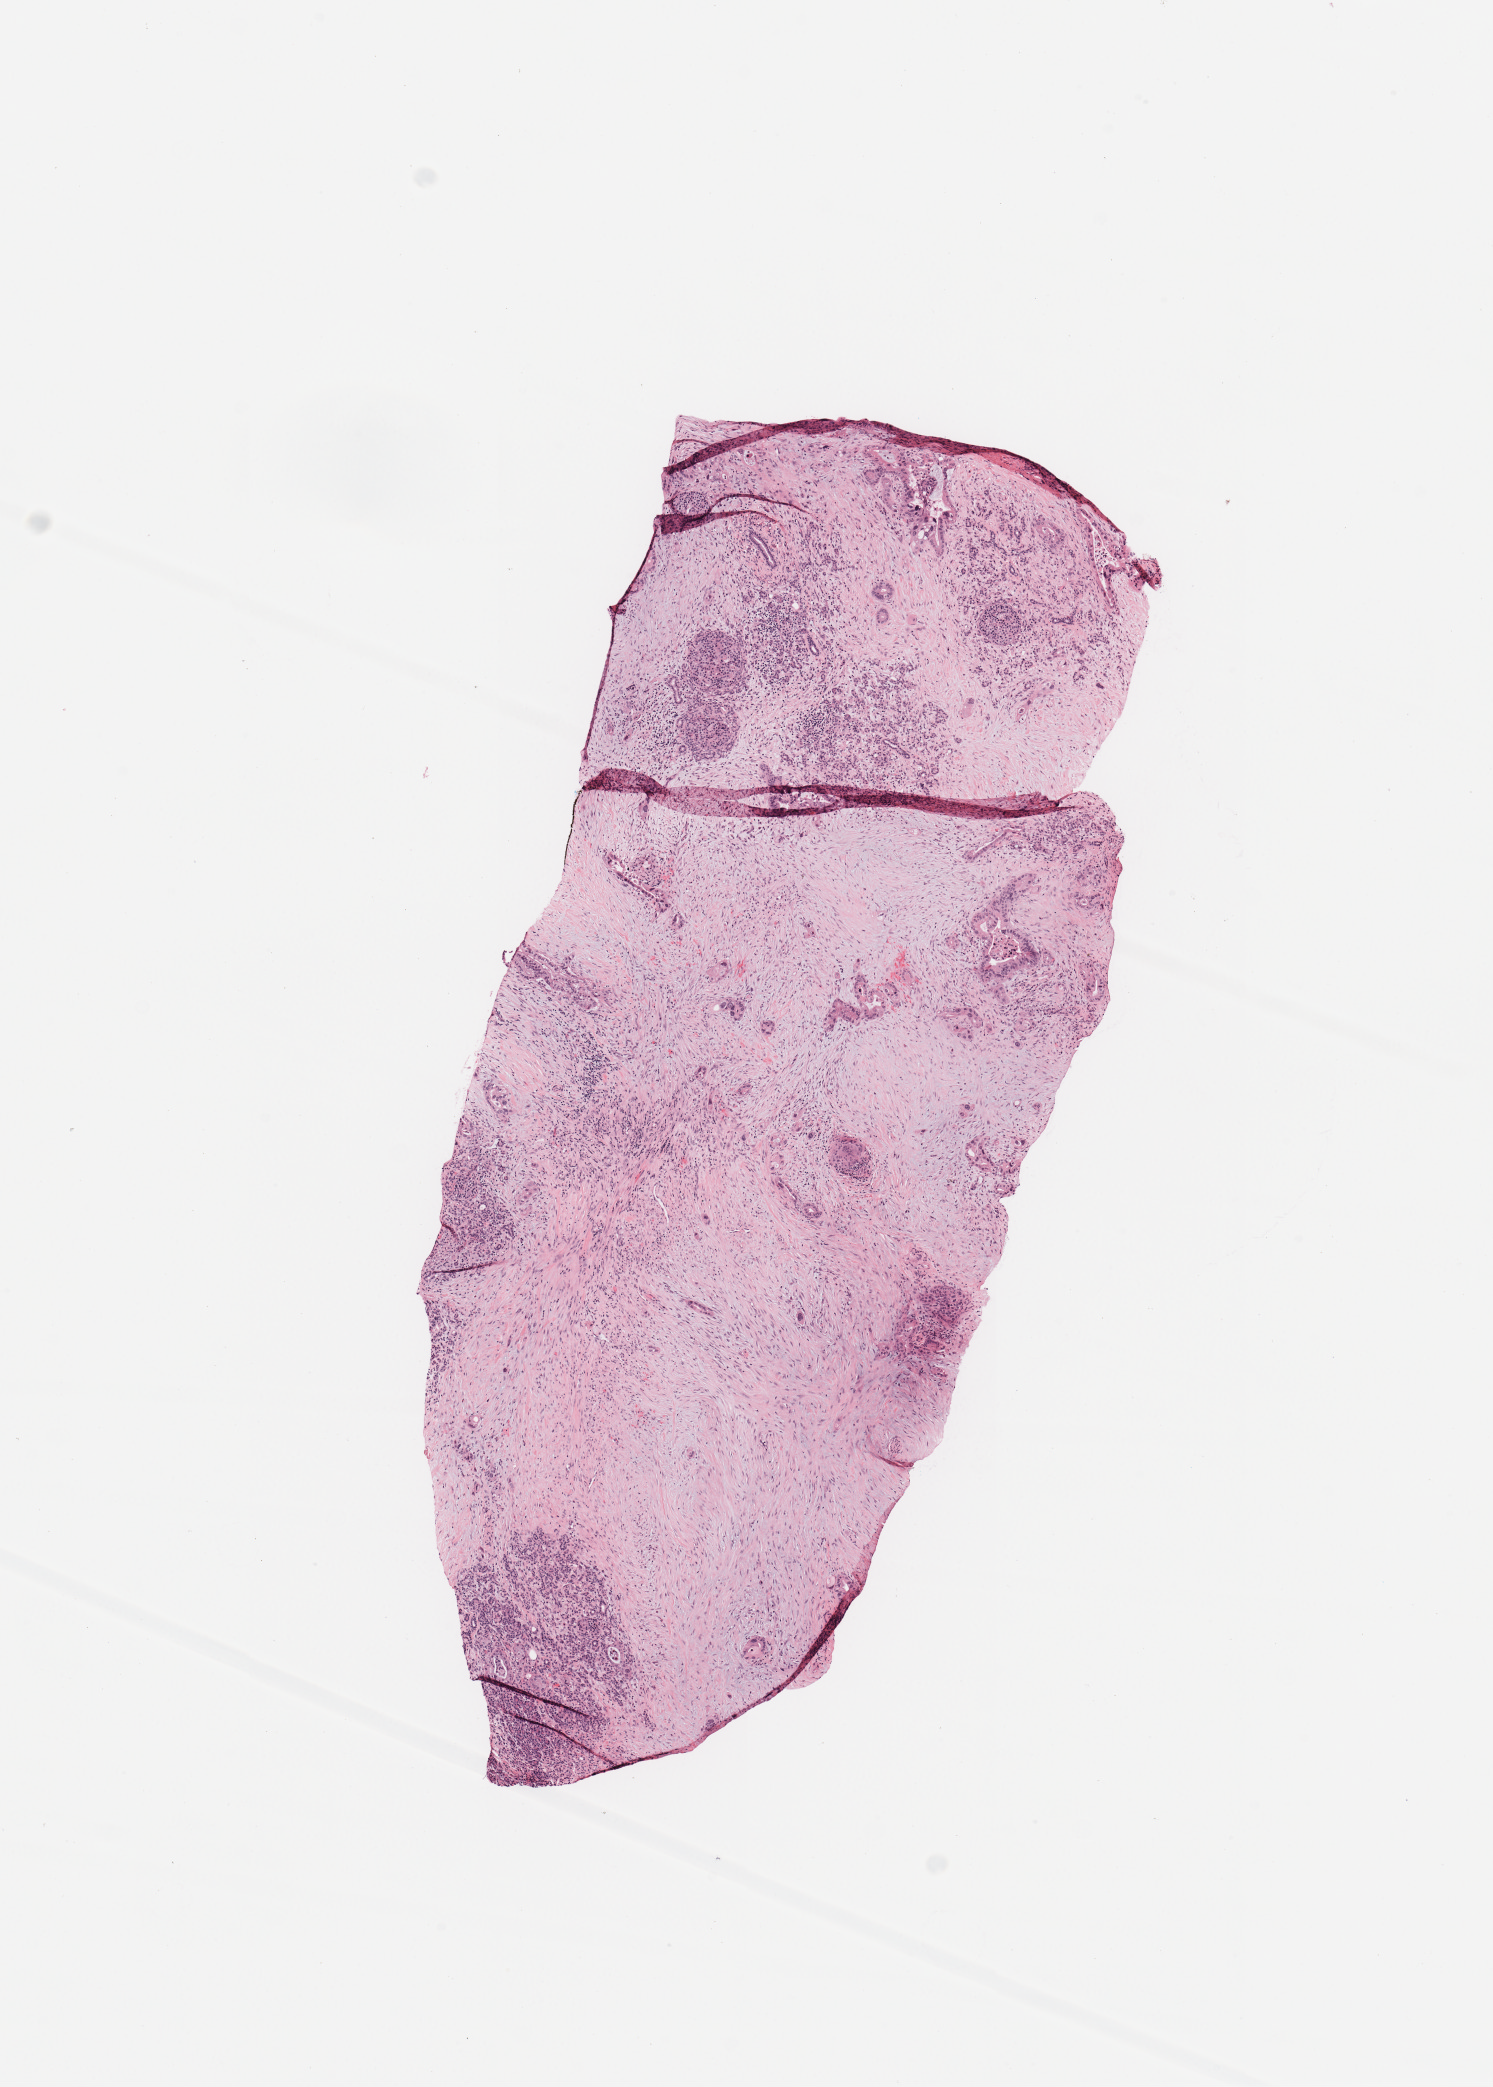
Whole-slide histology image, Hematoxylin and eosin (H&E) stained, a low-resolution overview of the entire scanned area, about 5.9 x 8.3 mm (acquisition: 20x scan); tumour tissue sample, sampled site: pancreas. 36-year-old female patient. Histologic grade: G2 (moderately differentiated). Composition of this section per pathologist review: tumour nuclei 10%, necrosis 0%.
AJCC pathologic stage: III. Histologic diagnosis: Infiltrating duct carcinoma, NOS.